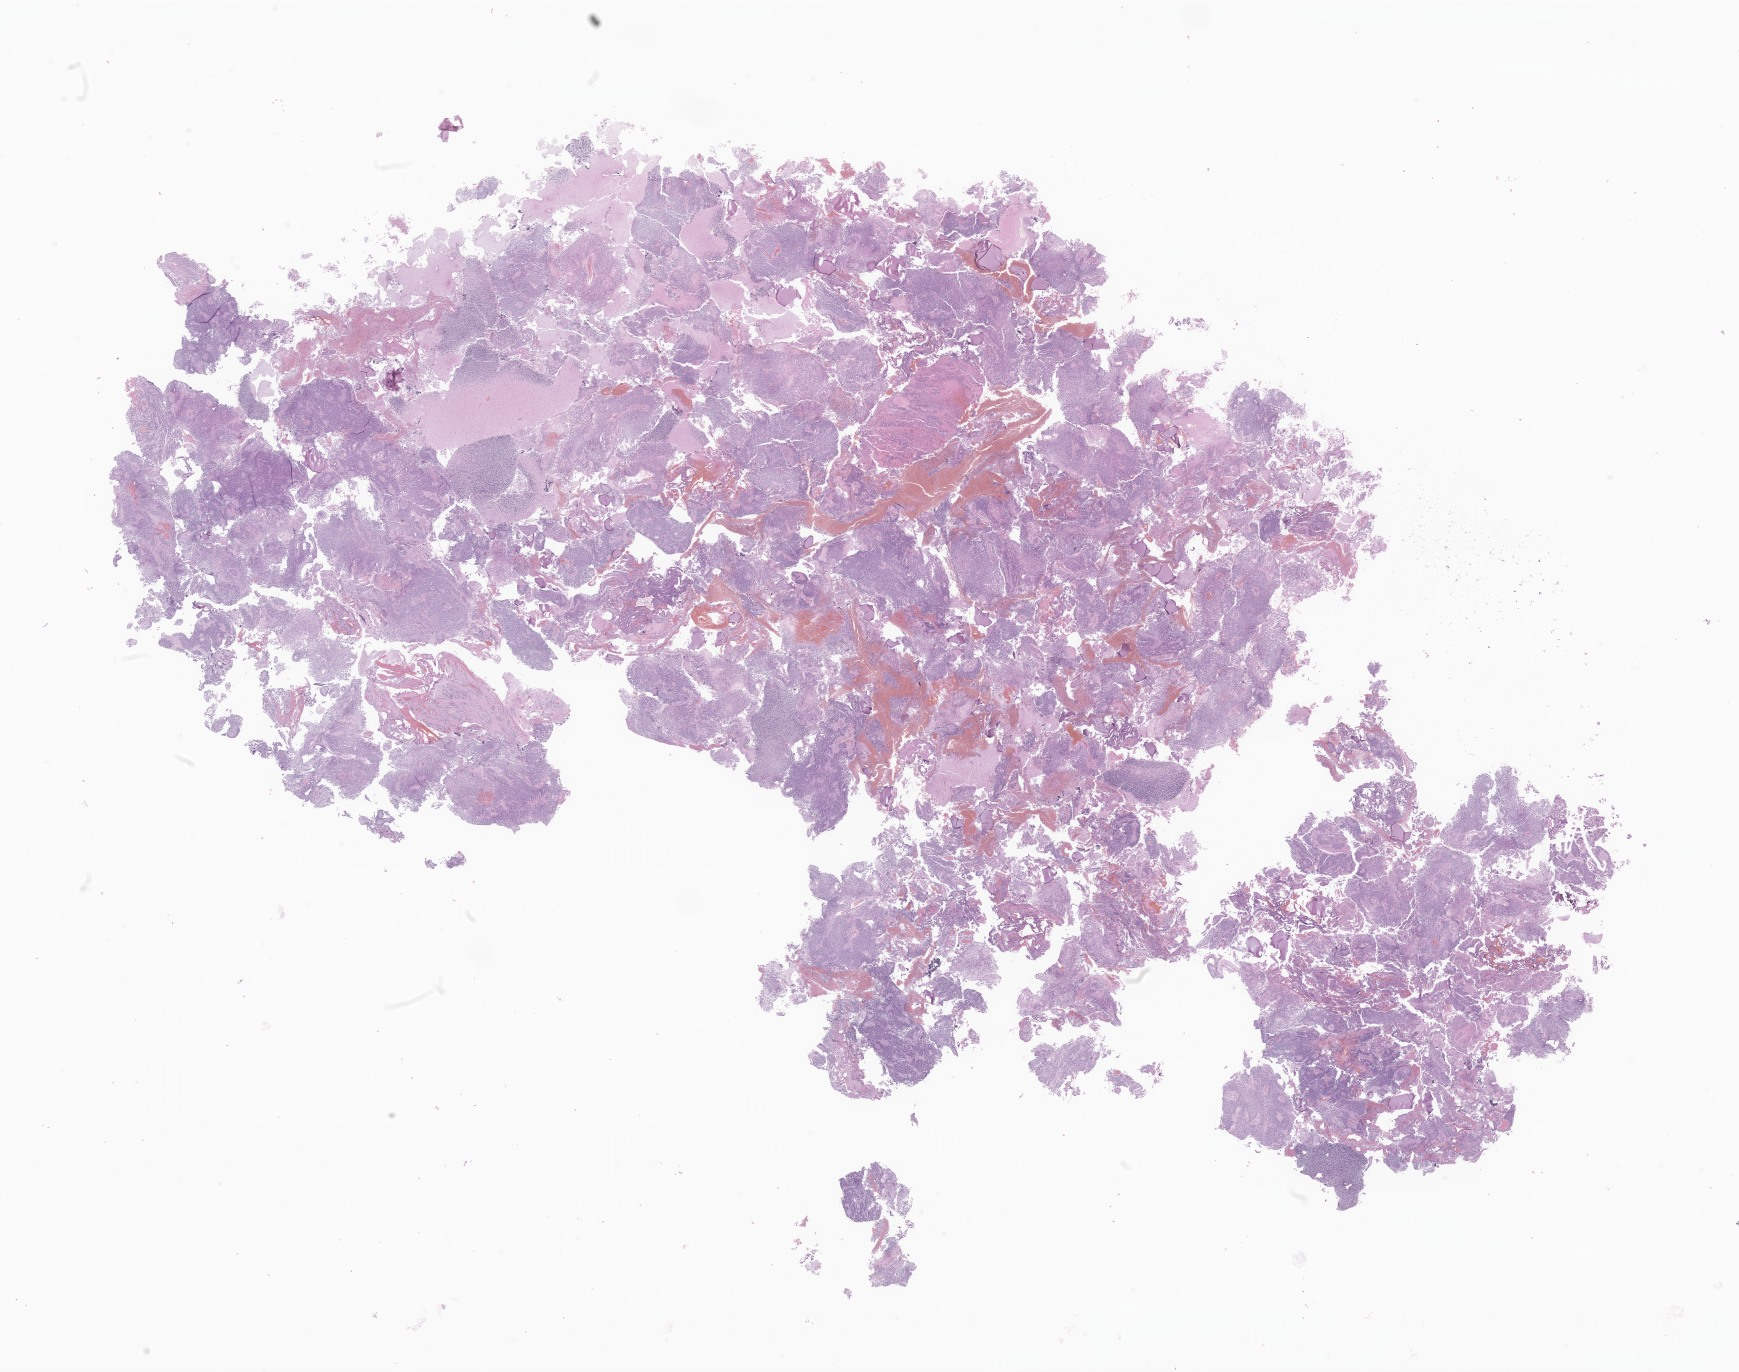
Digitized haematoxylin and eosin-stained section of tumor tissue from the brain — low-resolution overview of the scanned area, about 29.3 x 23.1 mm. FFPE section. Male patient, age 113 months (9 years 5 months).
- diagnosis: Ependymoma, NOS